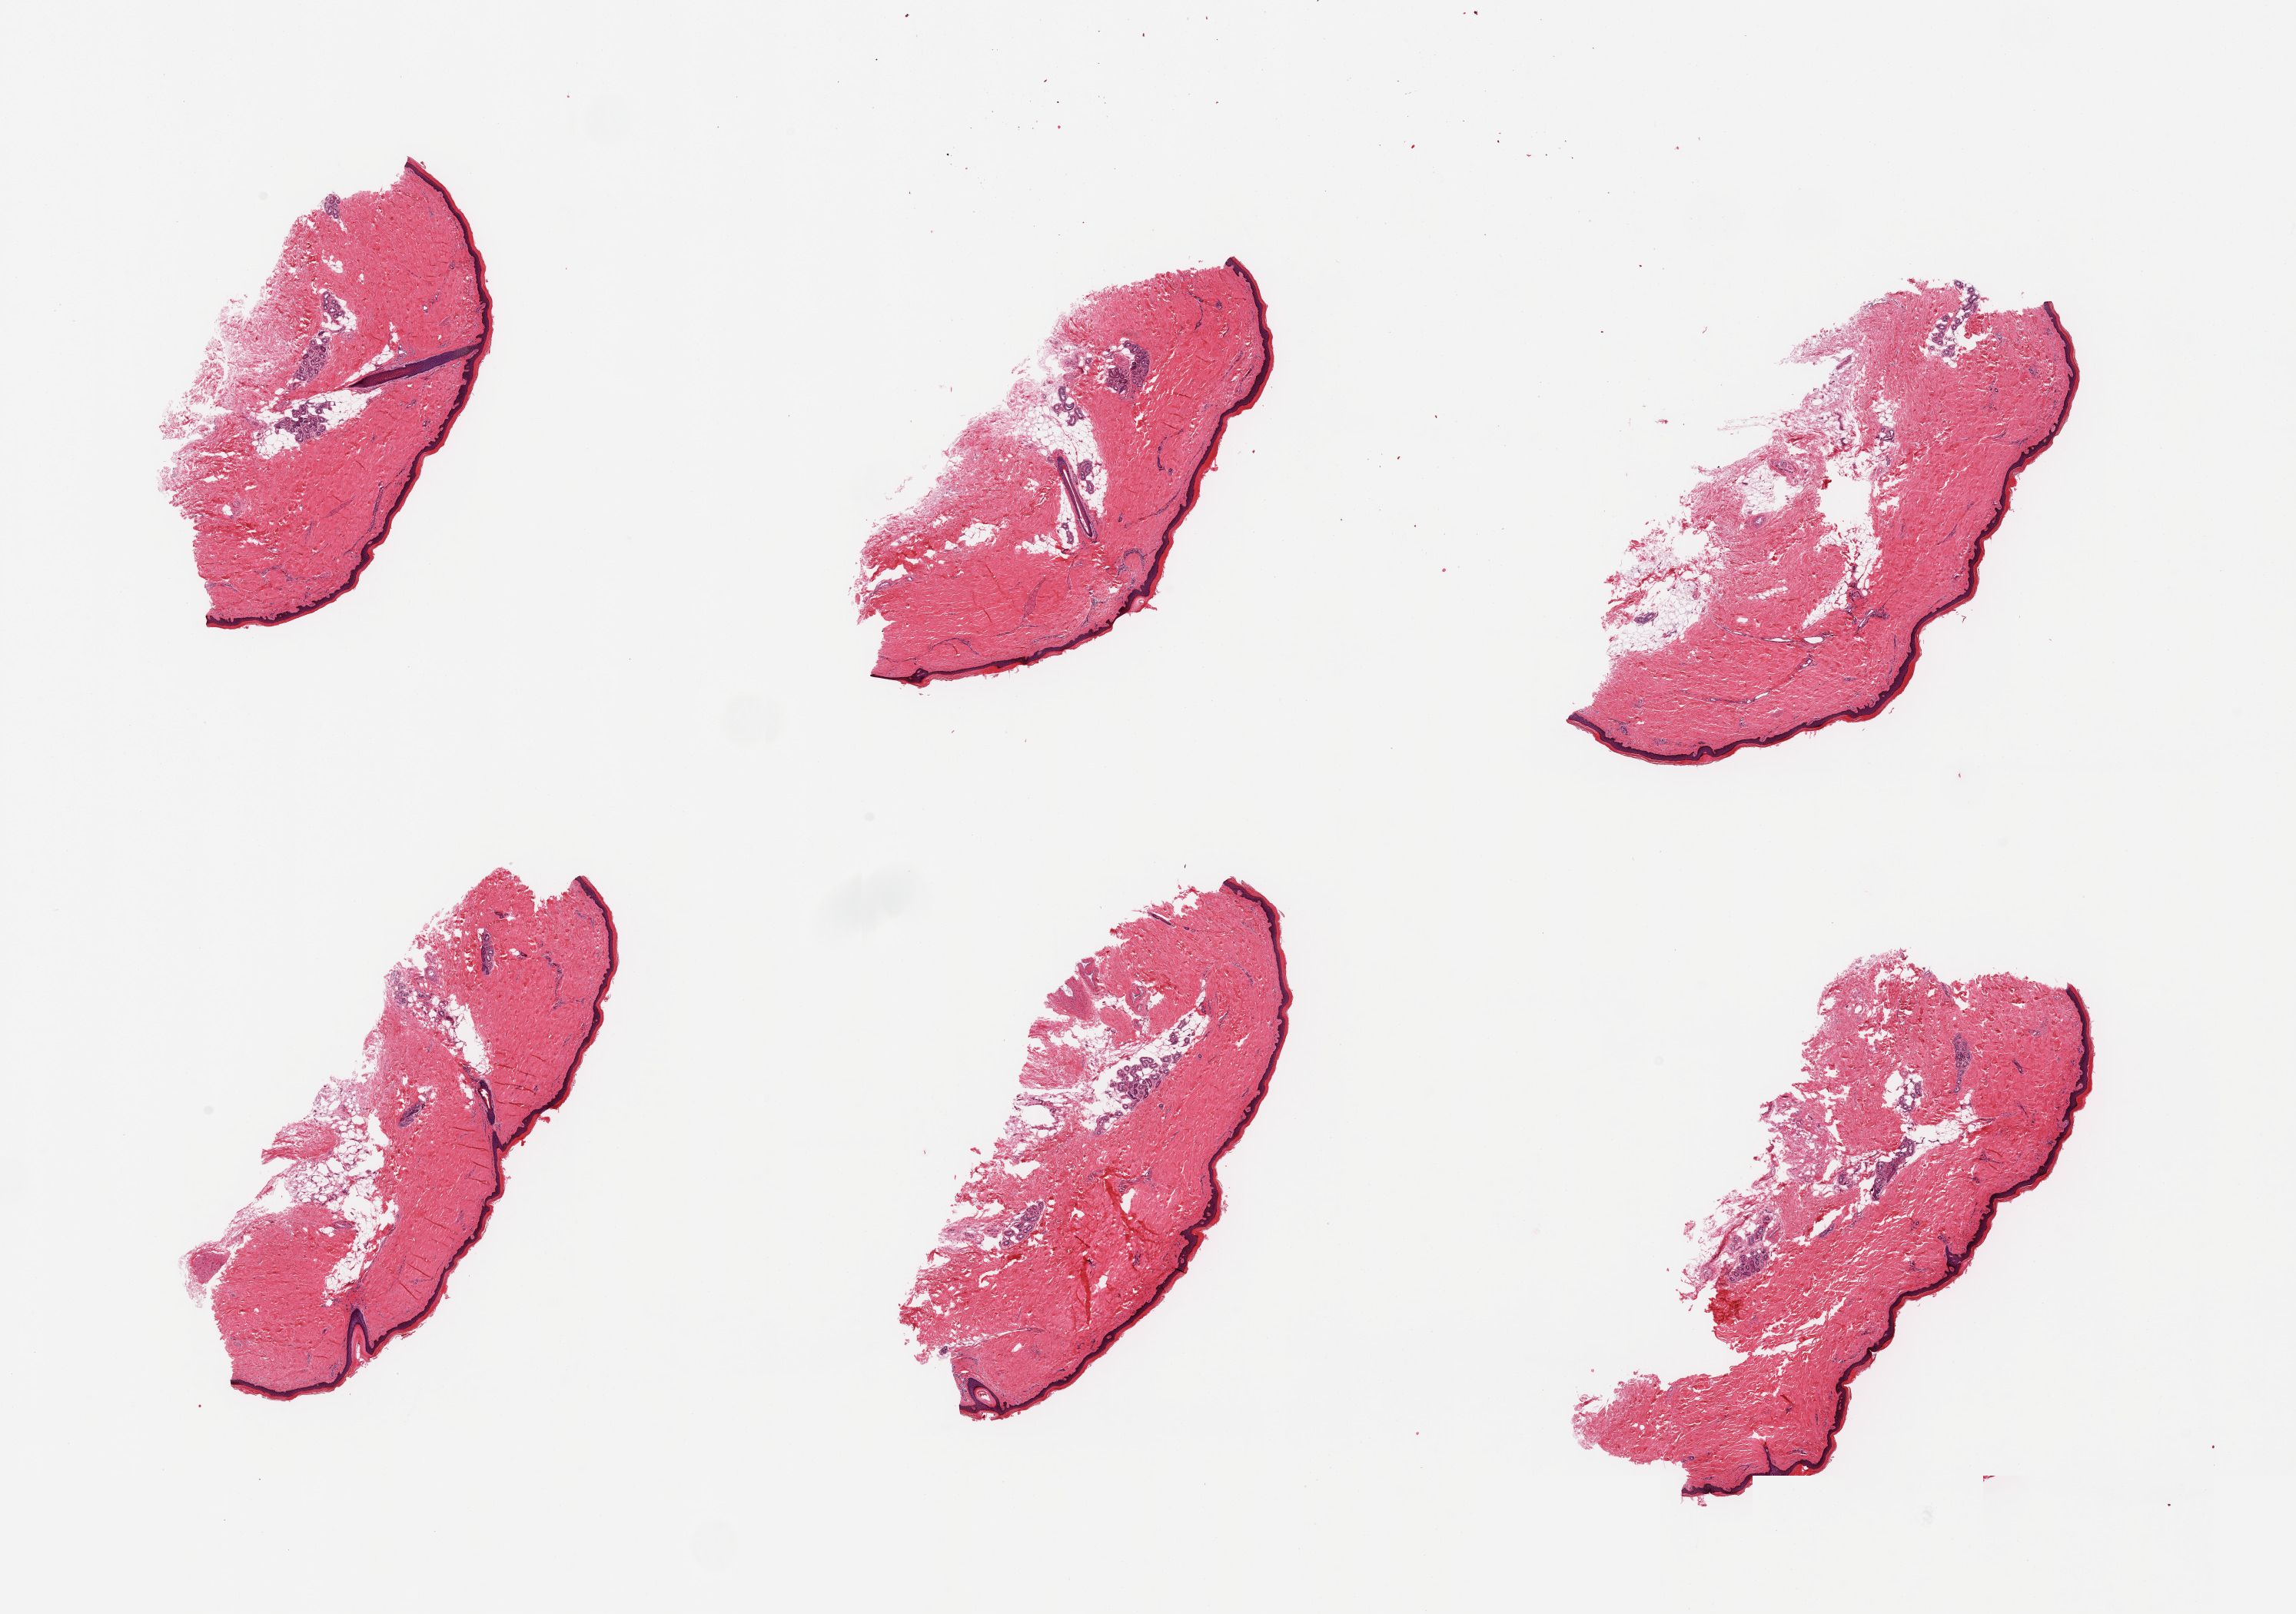
Whole-slide image, hematoxylin and eosin (H&E) stain — shown as a low-resolution overview of the whole scanned area (about 23.6 x 16.6 mm, from a 20x scan), PAXgene-fixed, paraffin-embedded tissue, target tissue: skin of lower leg, donor tissue sample.
Review note (as recorded): 6 pieces; ~5% to 10% dermal fat.